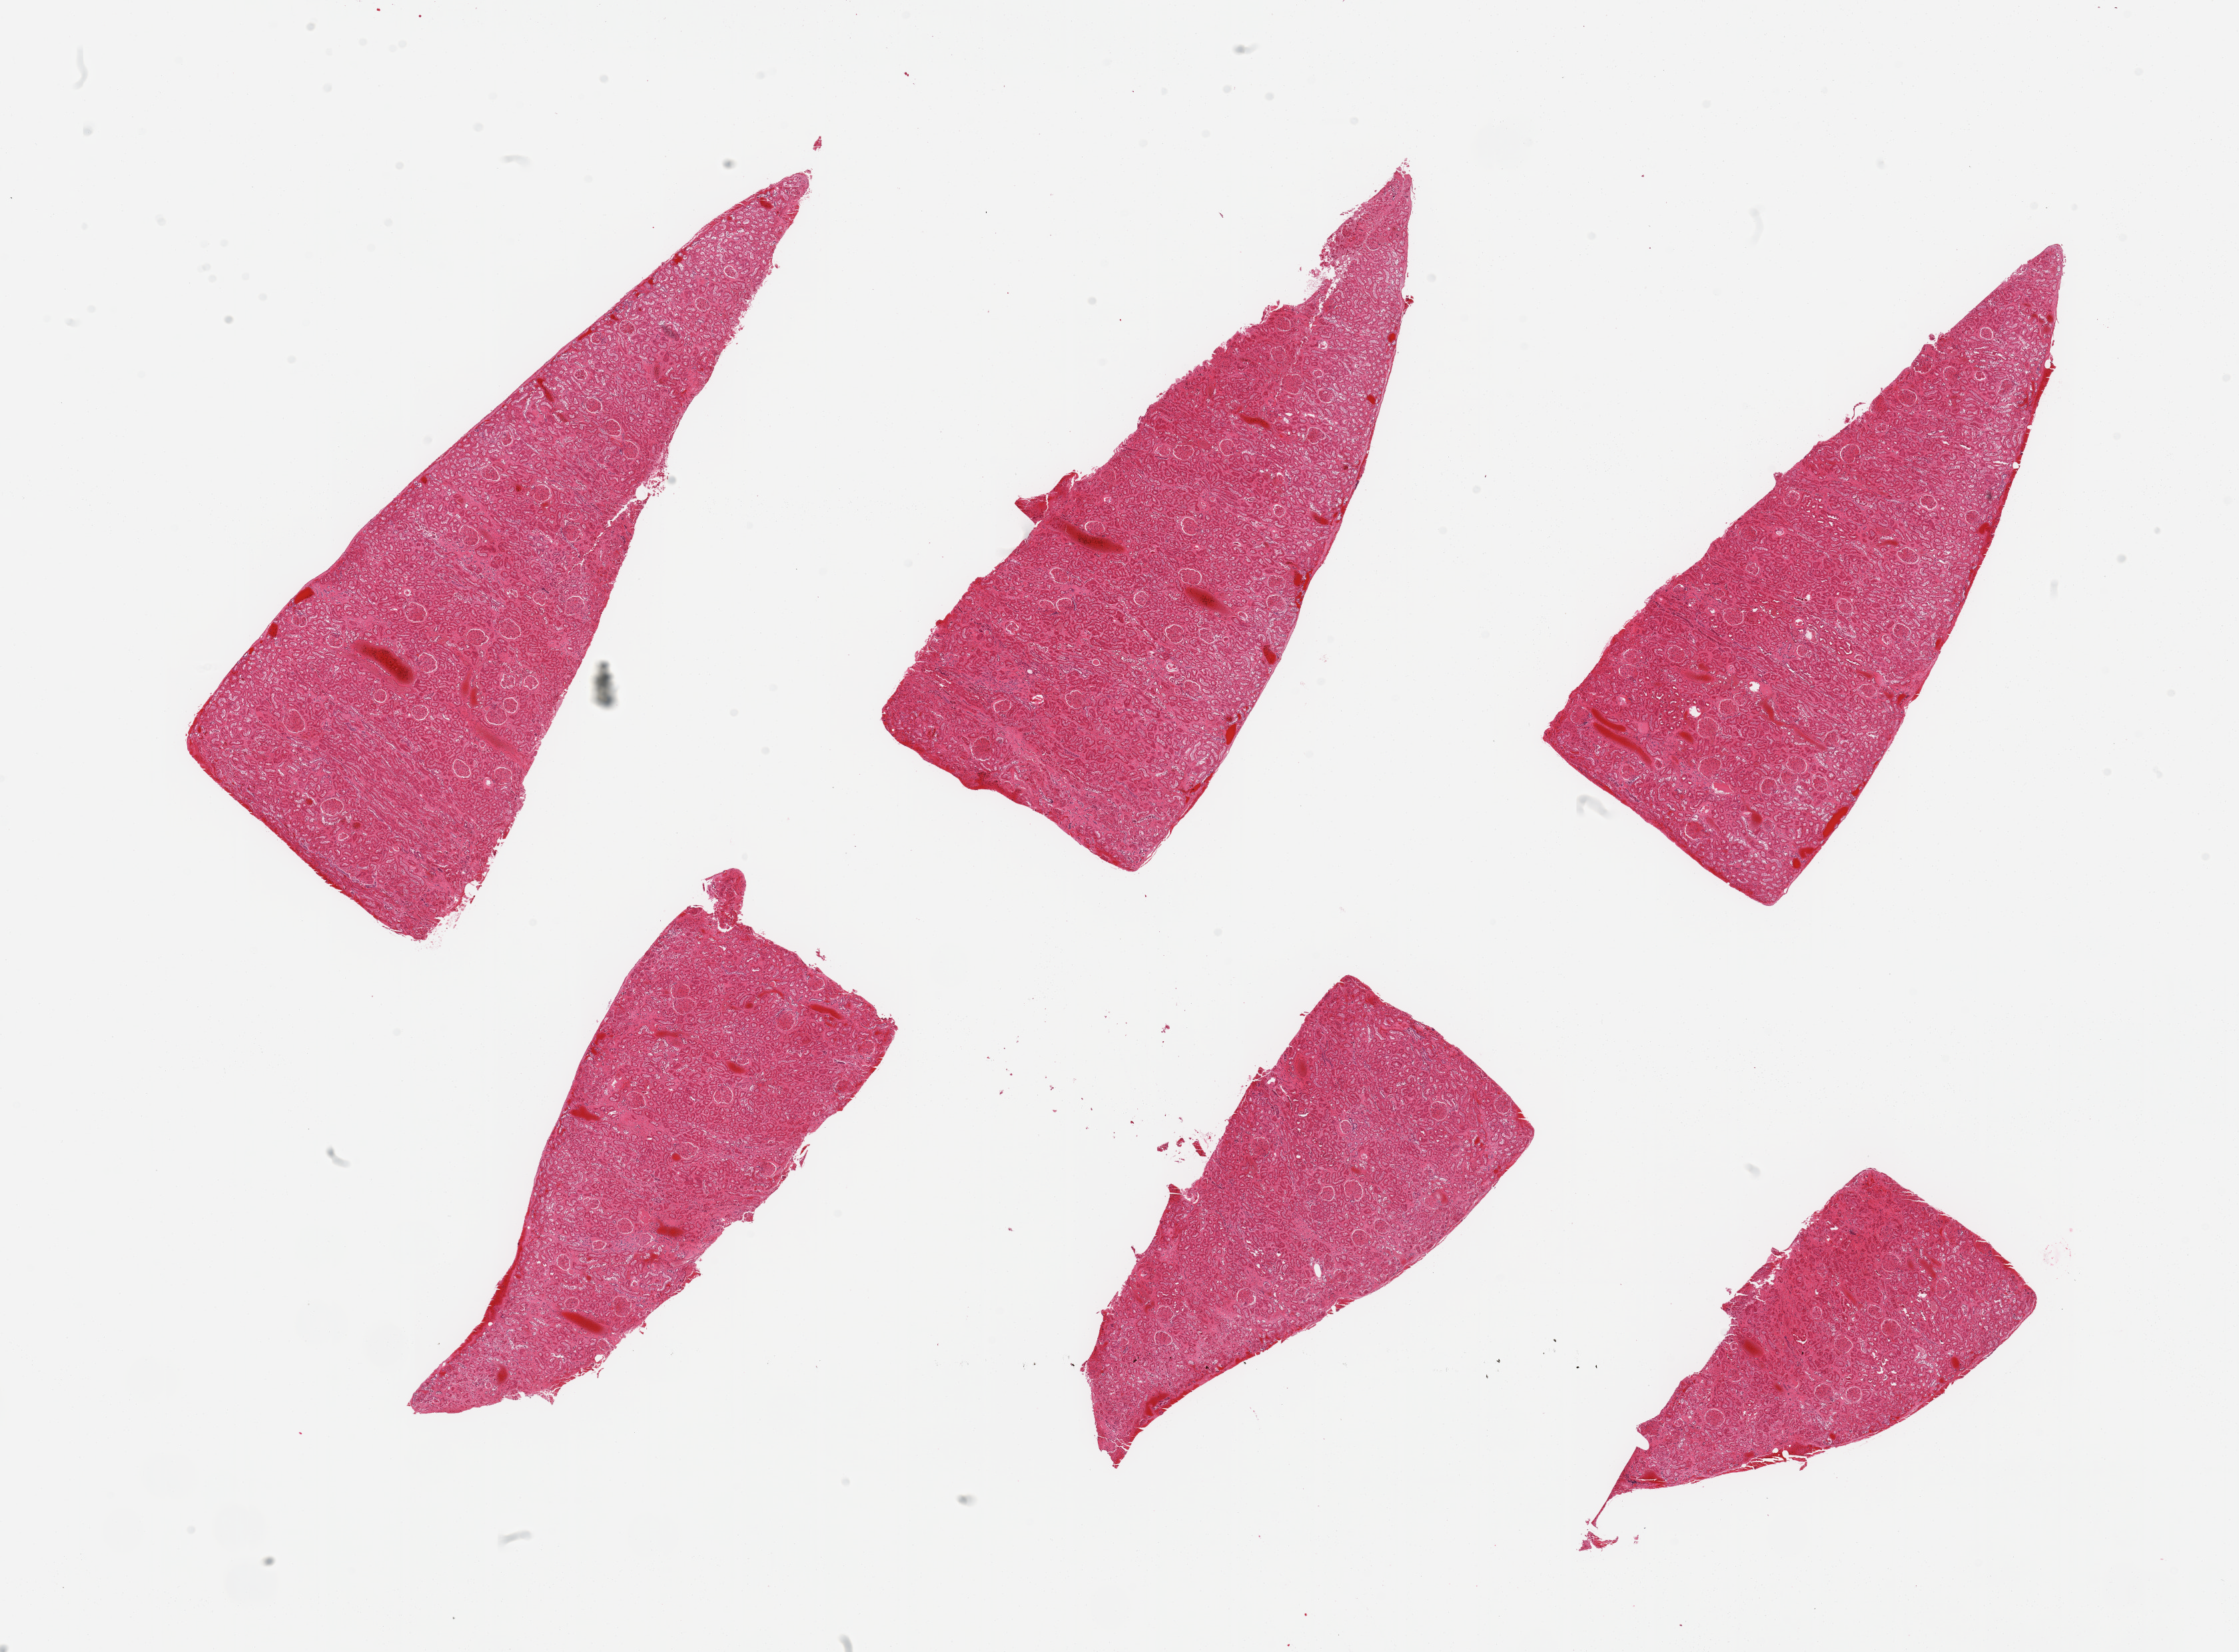
Haematoxylin and eosin whole-slide image, brightfield, low-resolution overview of the scanned area, about 26.6 x 19.6 mm (from a 20x scan); PAXgene-fixed, paraffin-embedded tissue; section of renal cortex (target tissue); tissue donor sample. Donor sex: male.
• review note (as recorded): 6 pieces; marked congestion; interstitial fibrosis and scarring